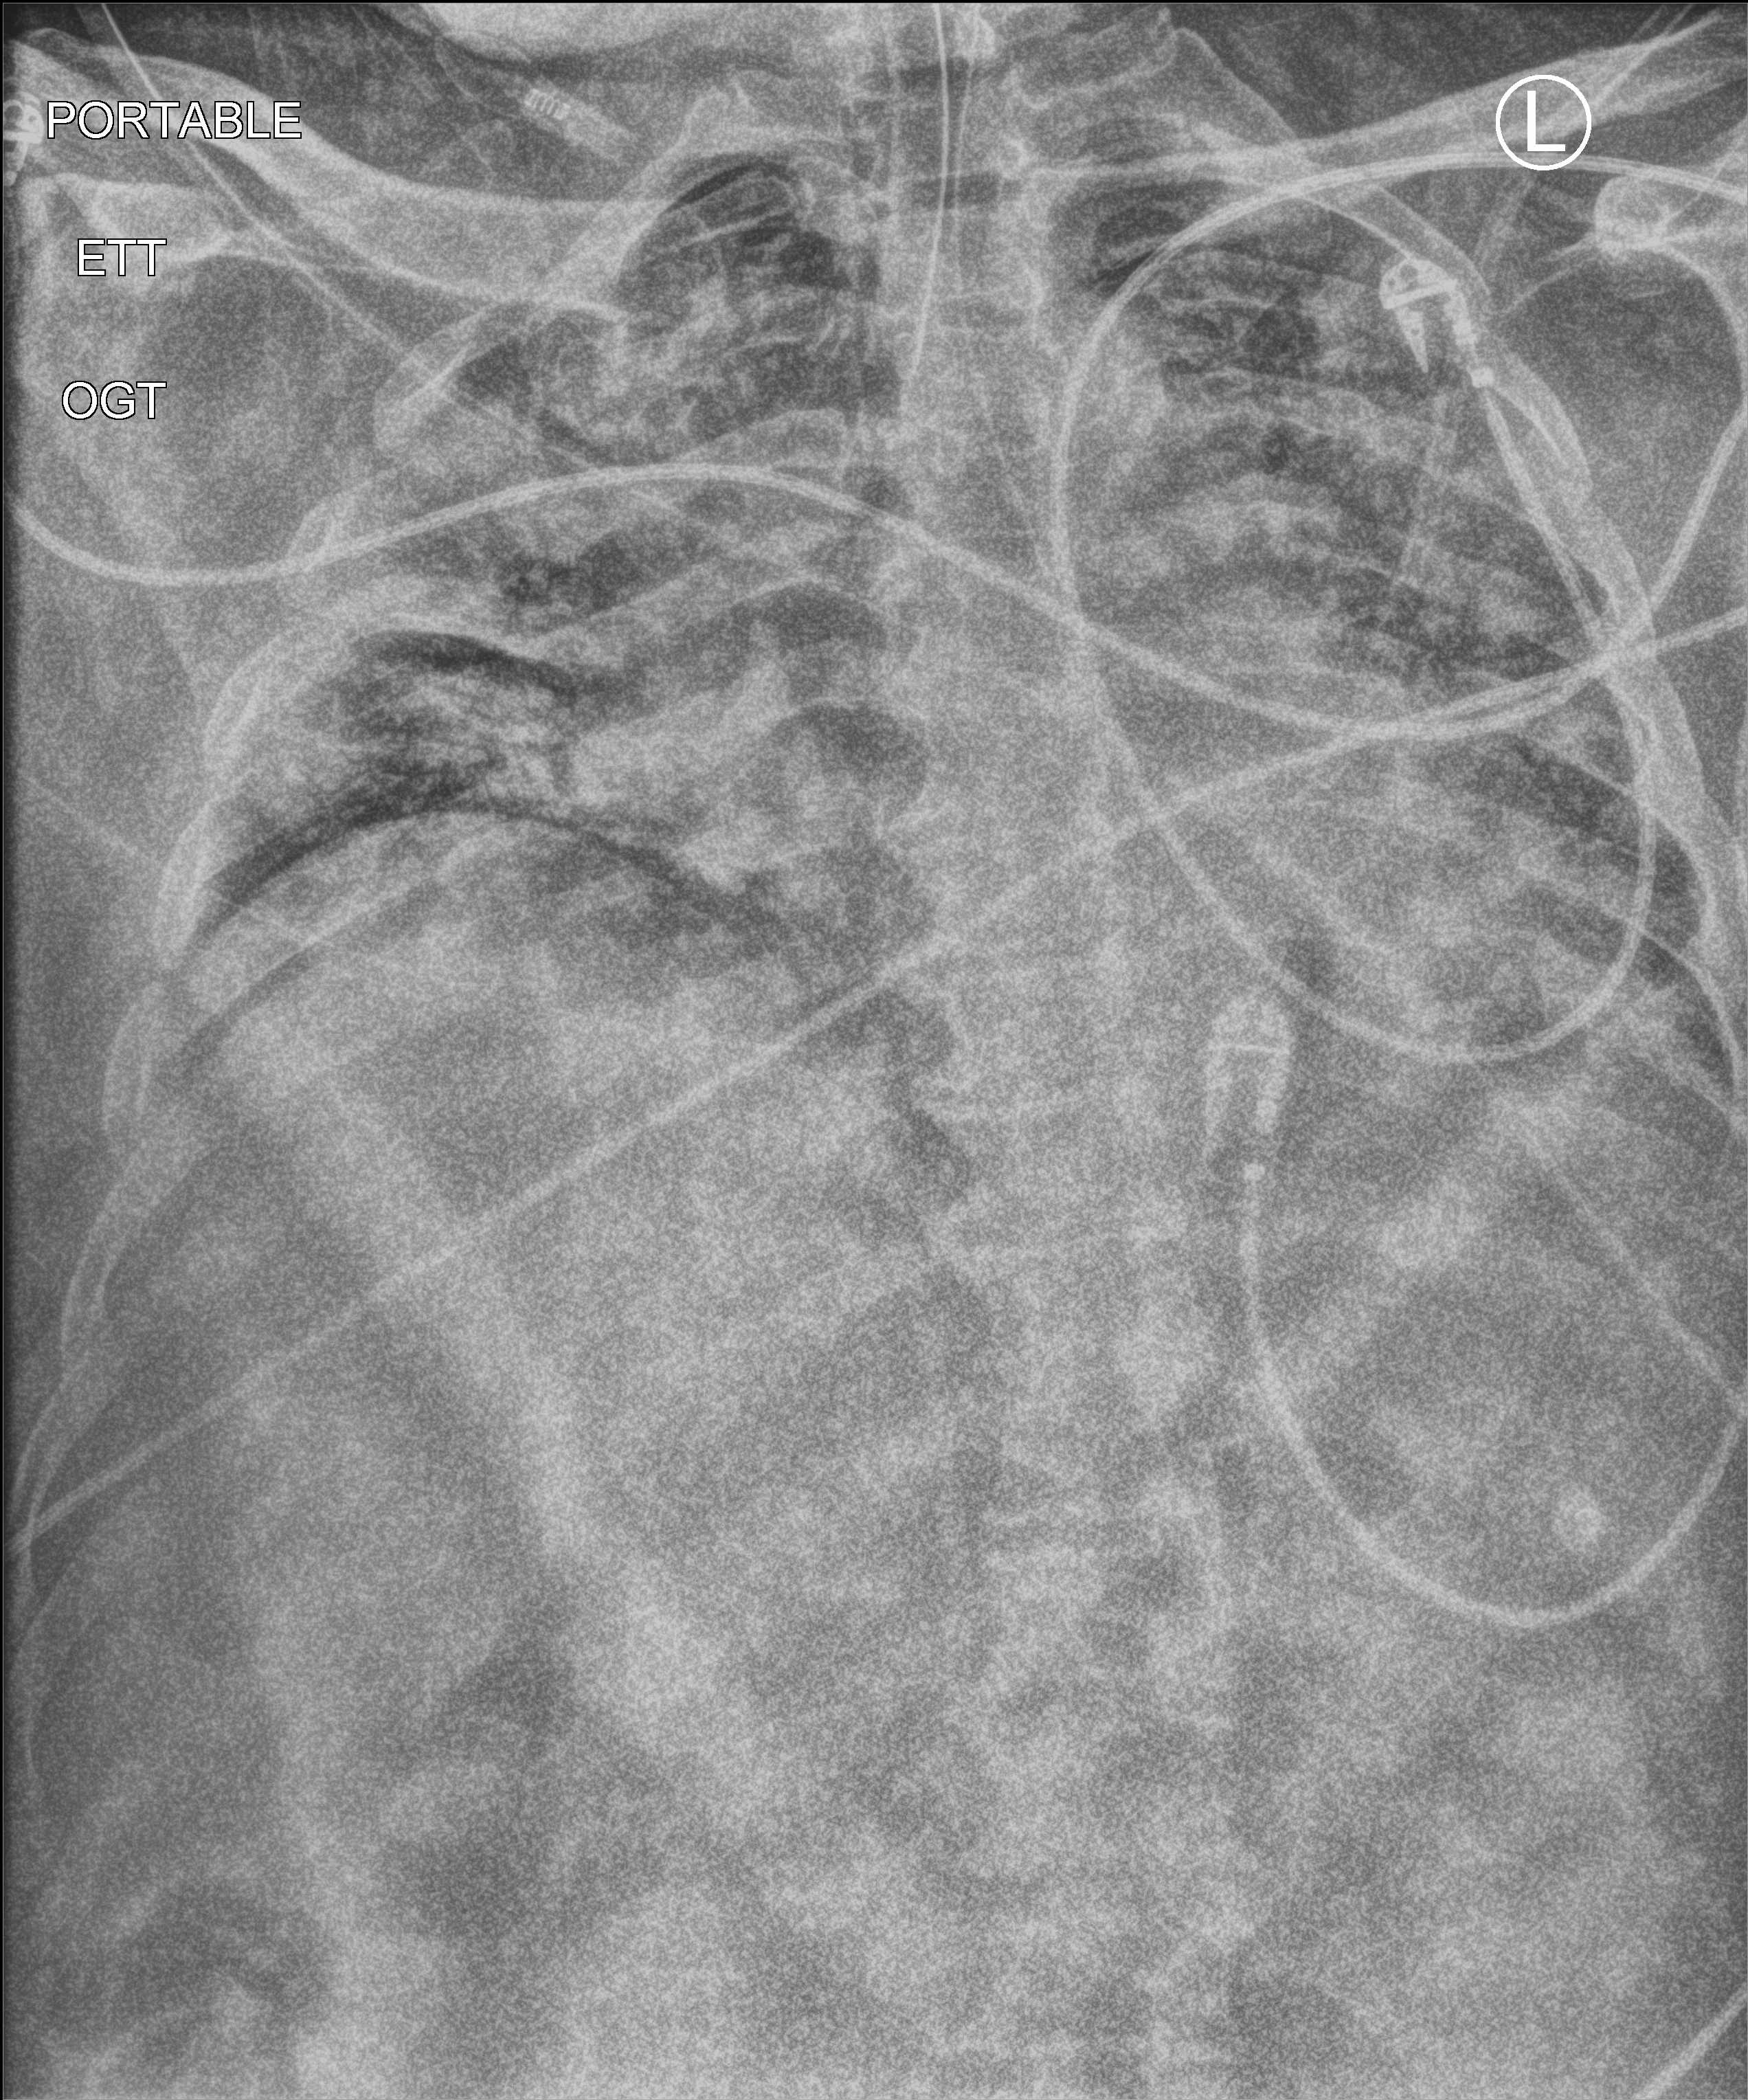
Portable chest radiograph, anteroposterior (AP) projection. Male patient hospitalised with COVID-19, age 60–74 years.
Hospital-stay facts (about this admission, not read from this image; timing relative to this image not recorded): length of hospital stay: 28 days; mechanically ventilated during this hospital stay: yes; admitted to intensive care during this hospital stay: yes.